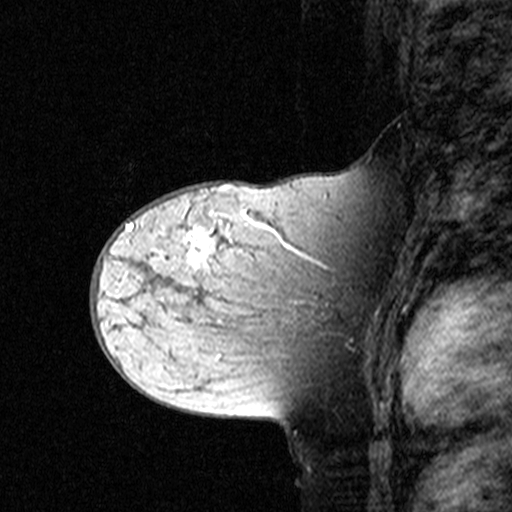
Breast MRI (dynamic contrast-enhanced), one sagittal slice; slice 23 of 44 in the series (ordered by position); dynamic contrast-enhanced study with each time point stored as its own series, time point 2 of 3 at this slice position (early post-contrast, ordered by acquisition time); 1.5 T; TE 4.5 ms, TR 11 ms; 512 × 512 image matrix. Patient: female, 44 years. Case-level facts recorded for this patient, not image findings: setting: breast cancer imaged before/during neoadjuvant chemotherapy; receptor status: triple-negative.
Outlined on this slice (semi-automatically segmented with operator editing):
- analysis volume of interest (the breast-tissue region the enhancement analysis was run in; not a lesion): bounding box [x1, y1, x2, y2] px = [142, 208, 349, 363]
- tumour enhancement mask (voxels above the 90 % enhancement threshold inside the analysis volume of interest): [189, 210, 247, 268]